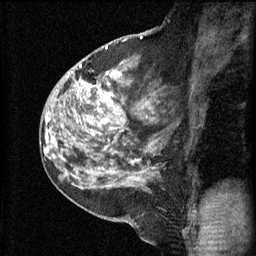
Breast MRI (dynamic contrast-enhanced), one sagittal slice. Slice 35 of 60 in the series (ordered by position). 3 images stored at this slice position (order not interpretable as contrast timing). 1.5 T. TE 4.2 ms, TR 11 ms. 256 × 256 image matrix, field of view 180 × 180 mm. Female patient, age 52 years.
Outlined on this slice (semi-automatic segmentation, software-assisted and operator-edited):
- analysis volume of interest (the breast-tissue region the enhancement analysis was run in; not a lesion): bounding box (x1, y1, x2, y2) in pixels: (86, 76, 164, 157)
- tumour enhancement mask (voxels above the 70 % enhancement threshold inside the analysis volume of interest): (101, 76, 116, 125)